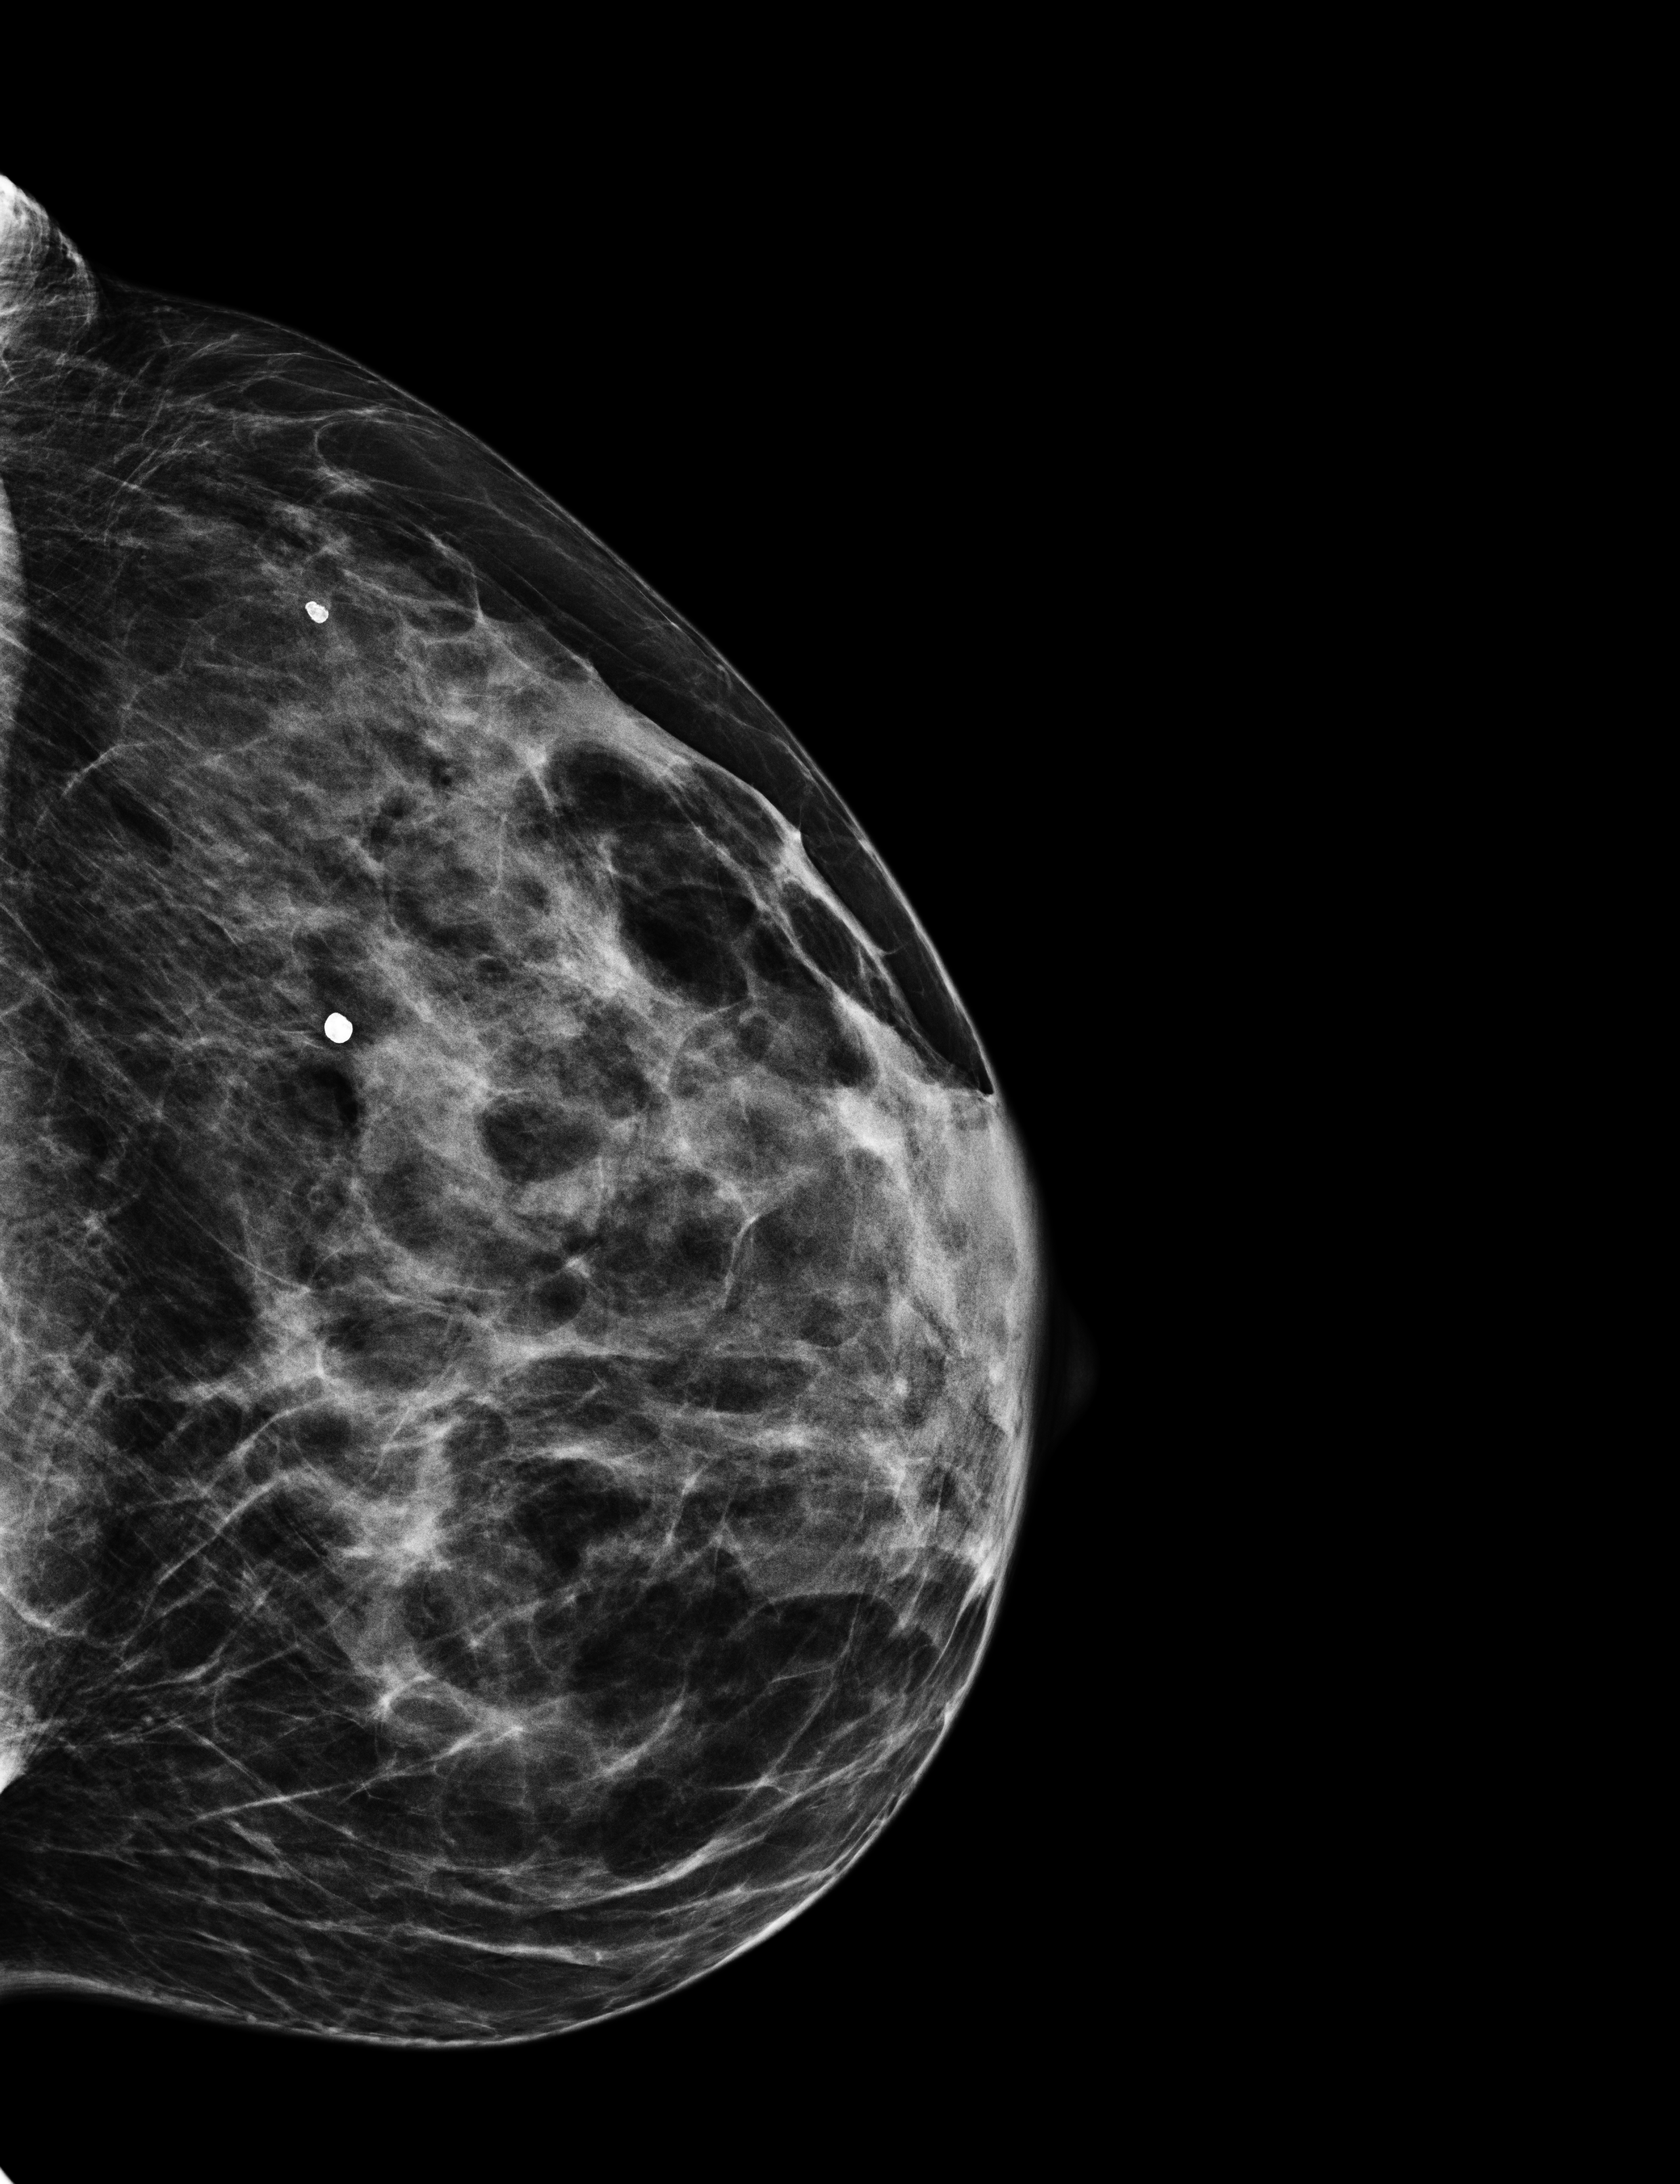
Full-field digital mammogram (FFDM); left breast; craniocaudal (CC) view; annual screening mammography examination; compressed breast thickness 38 mm. Patient aged 54 years (female).
- breast density at the screening exam (both breasts): heterogeneously dense (BI-RADS density category c)
- final BI-RADS category for the screening round (tomosynthesis exam, both breasts): category 1
- recall: no recall after this screen